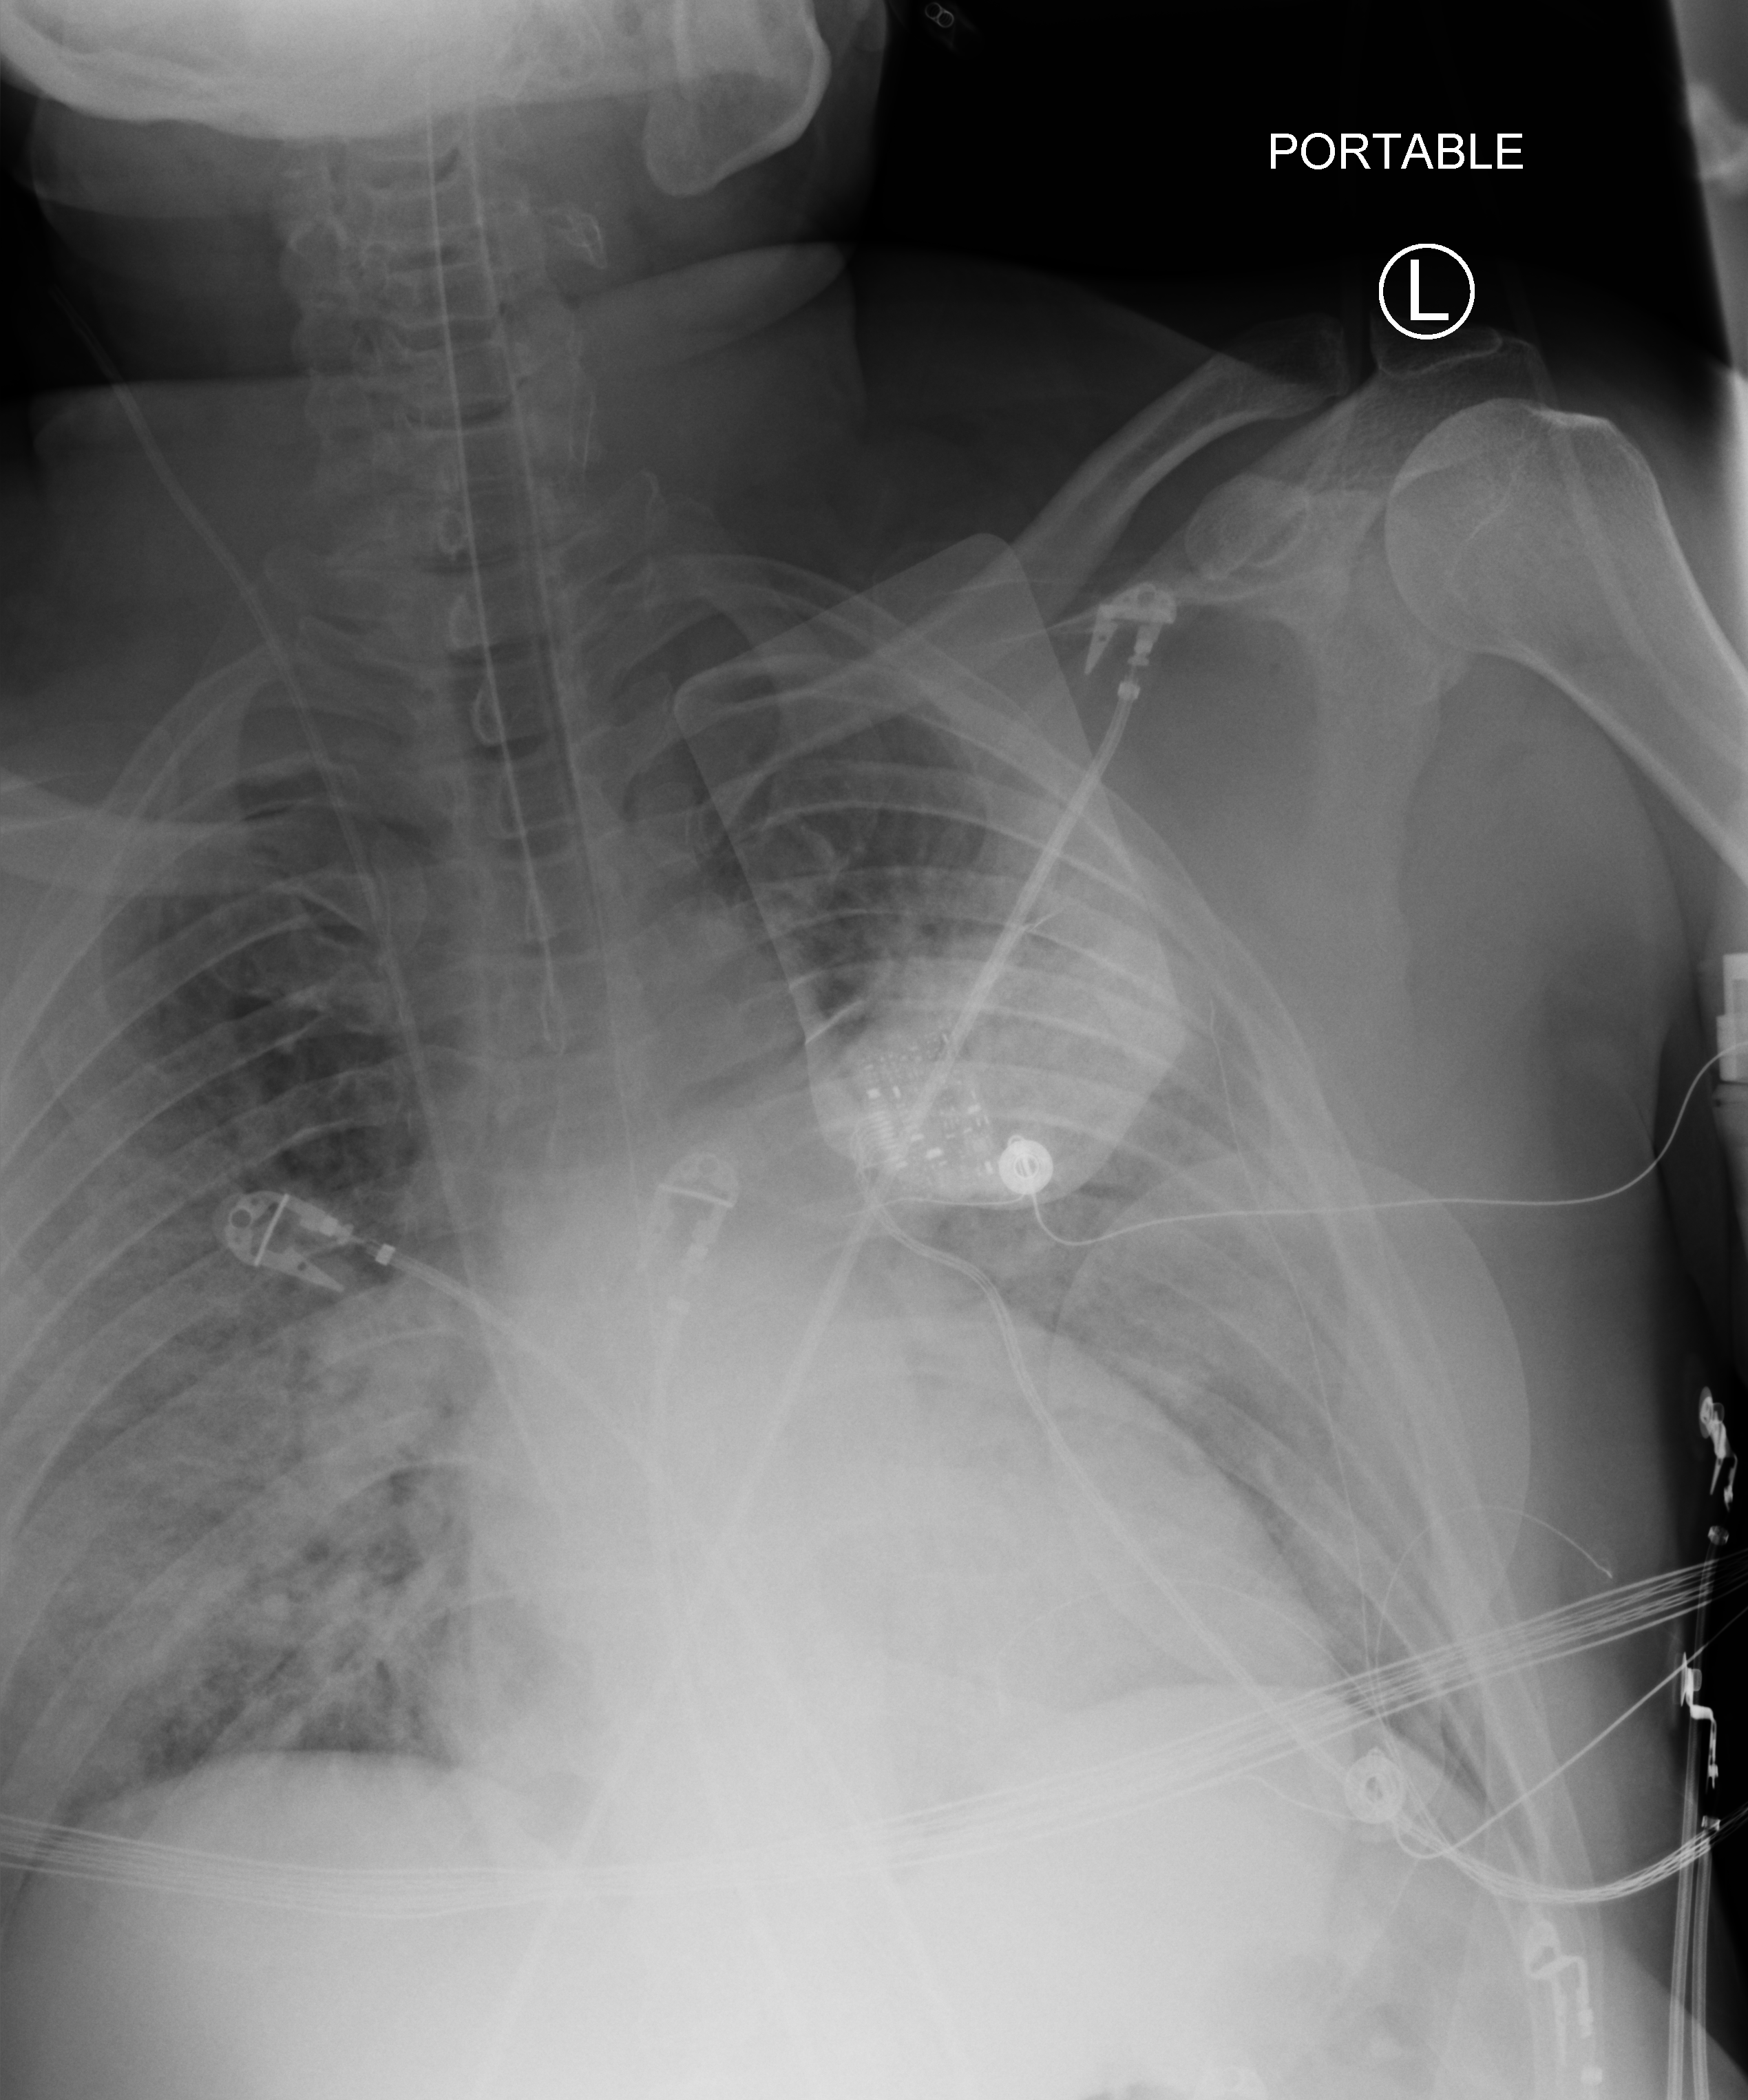
Portable chest radiograph, anteroposterior (AP) projection. Male patient hospitalised with COVID-19, age 18–59 years.
From the hospital-stay record, not from the radiograph (when in the stay this image was taken is not recorded): mechanically ventilated during this hospital stay: yes; length of hospital stay: 75 days.